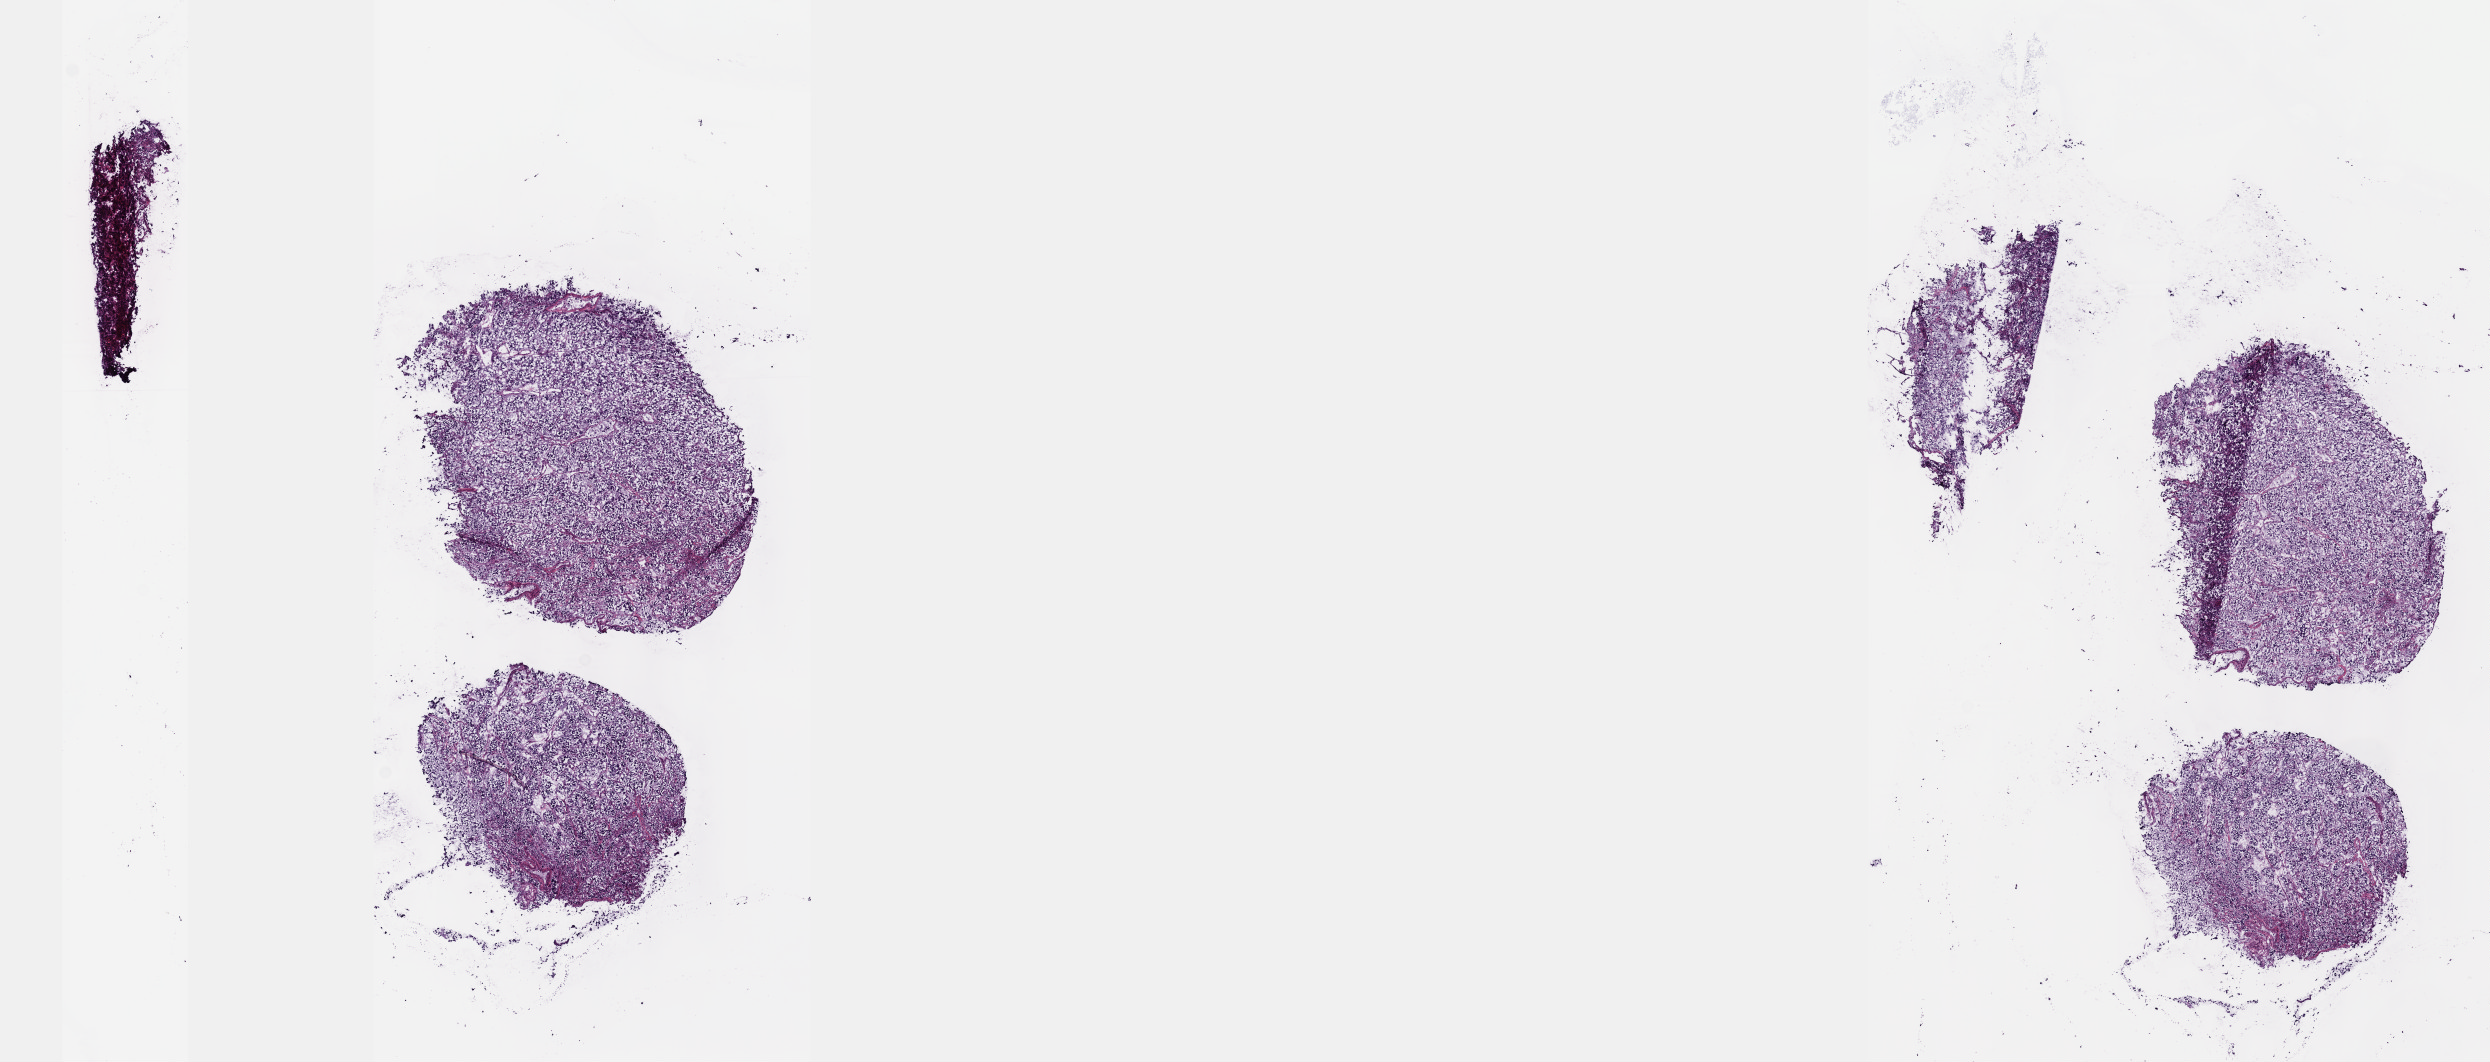
Digitized H&E-stained tissue section (whole slide), whole scanned area (about 20.1 x 8.6 mm) shown as a low-resolution overview. Frozen section from the top of the tissue portion. Primary tumour sample from the adrenal gland. Patient: male, age at initial diagnosis 25 years. Composition of this section per pathologist review: tumour cells 80%, tumour nuclei 80%, normal cells 0%, stromal cells 20%, necrosis 0%. Inflammatory infiltration, as recorded: lymphocyte infiltration 0%, monocyte infiltration 0%, neutrophil infiltration 0%.
Laterality: left. Pathologic diagnosis: Pheochromocytoma, NOS.